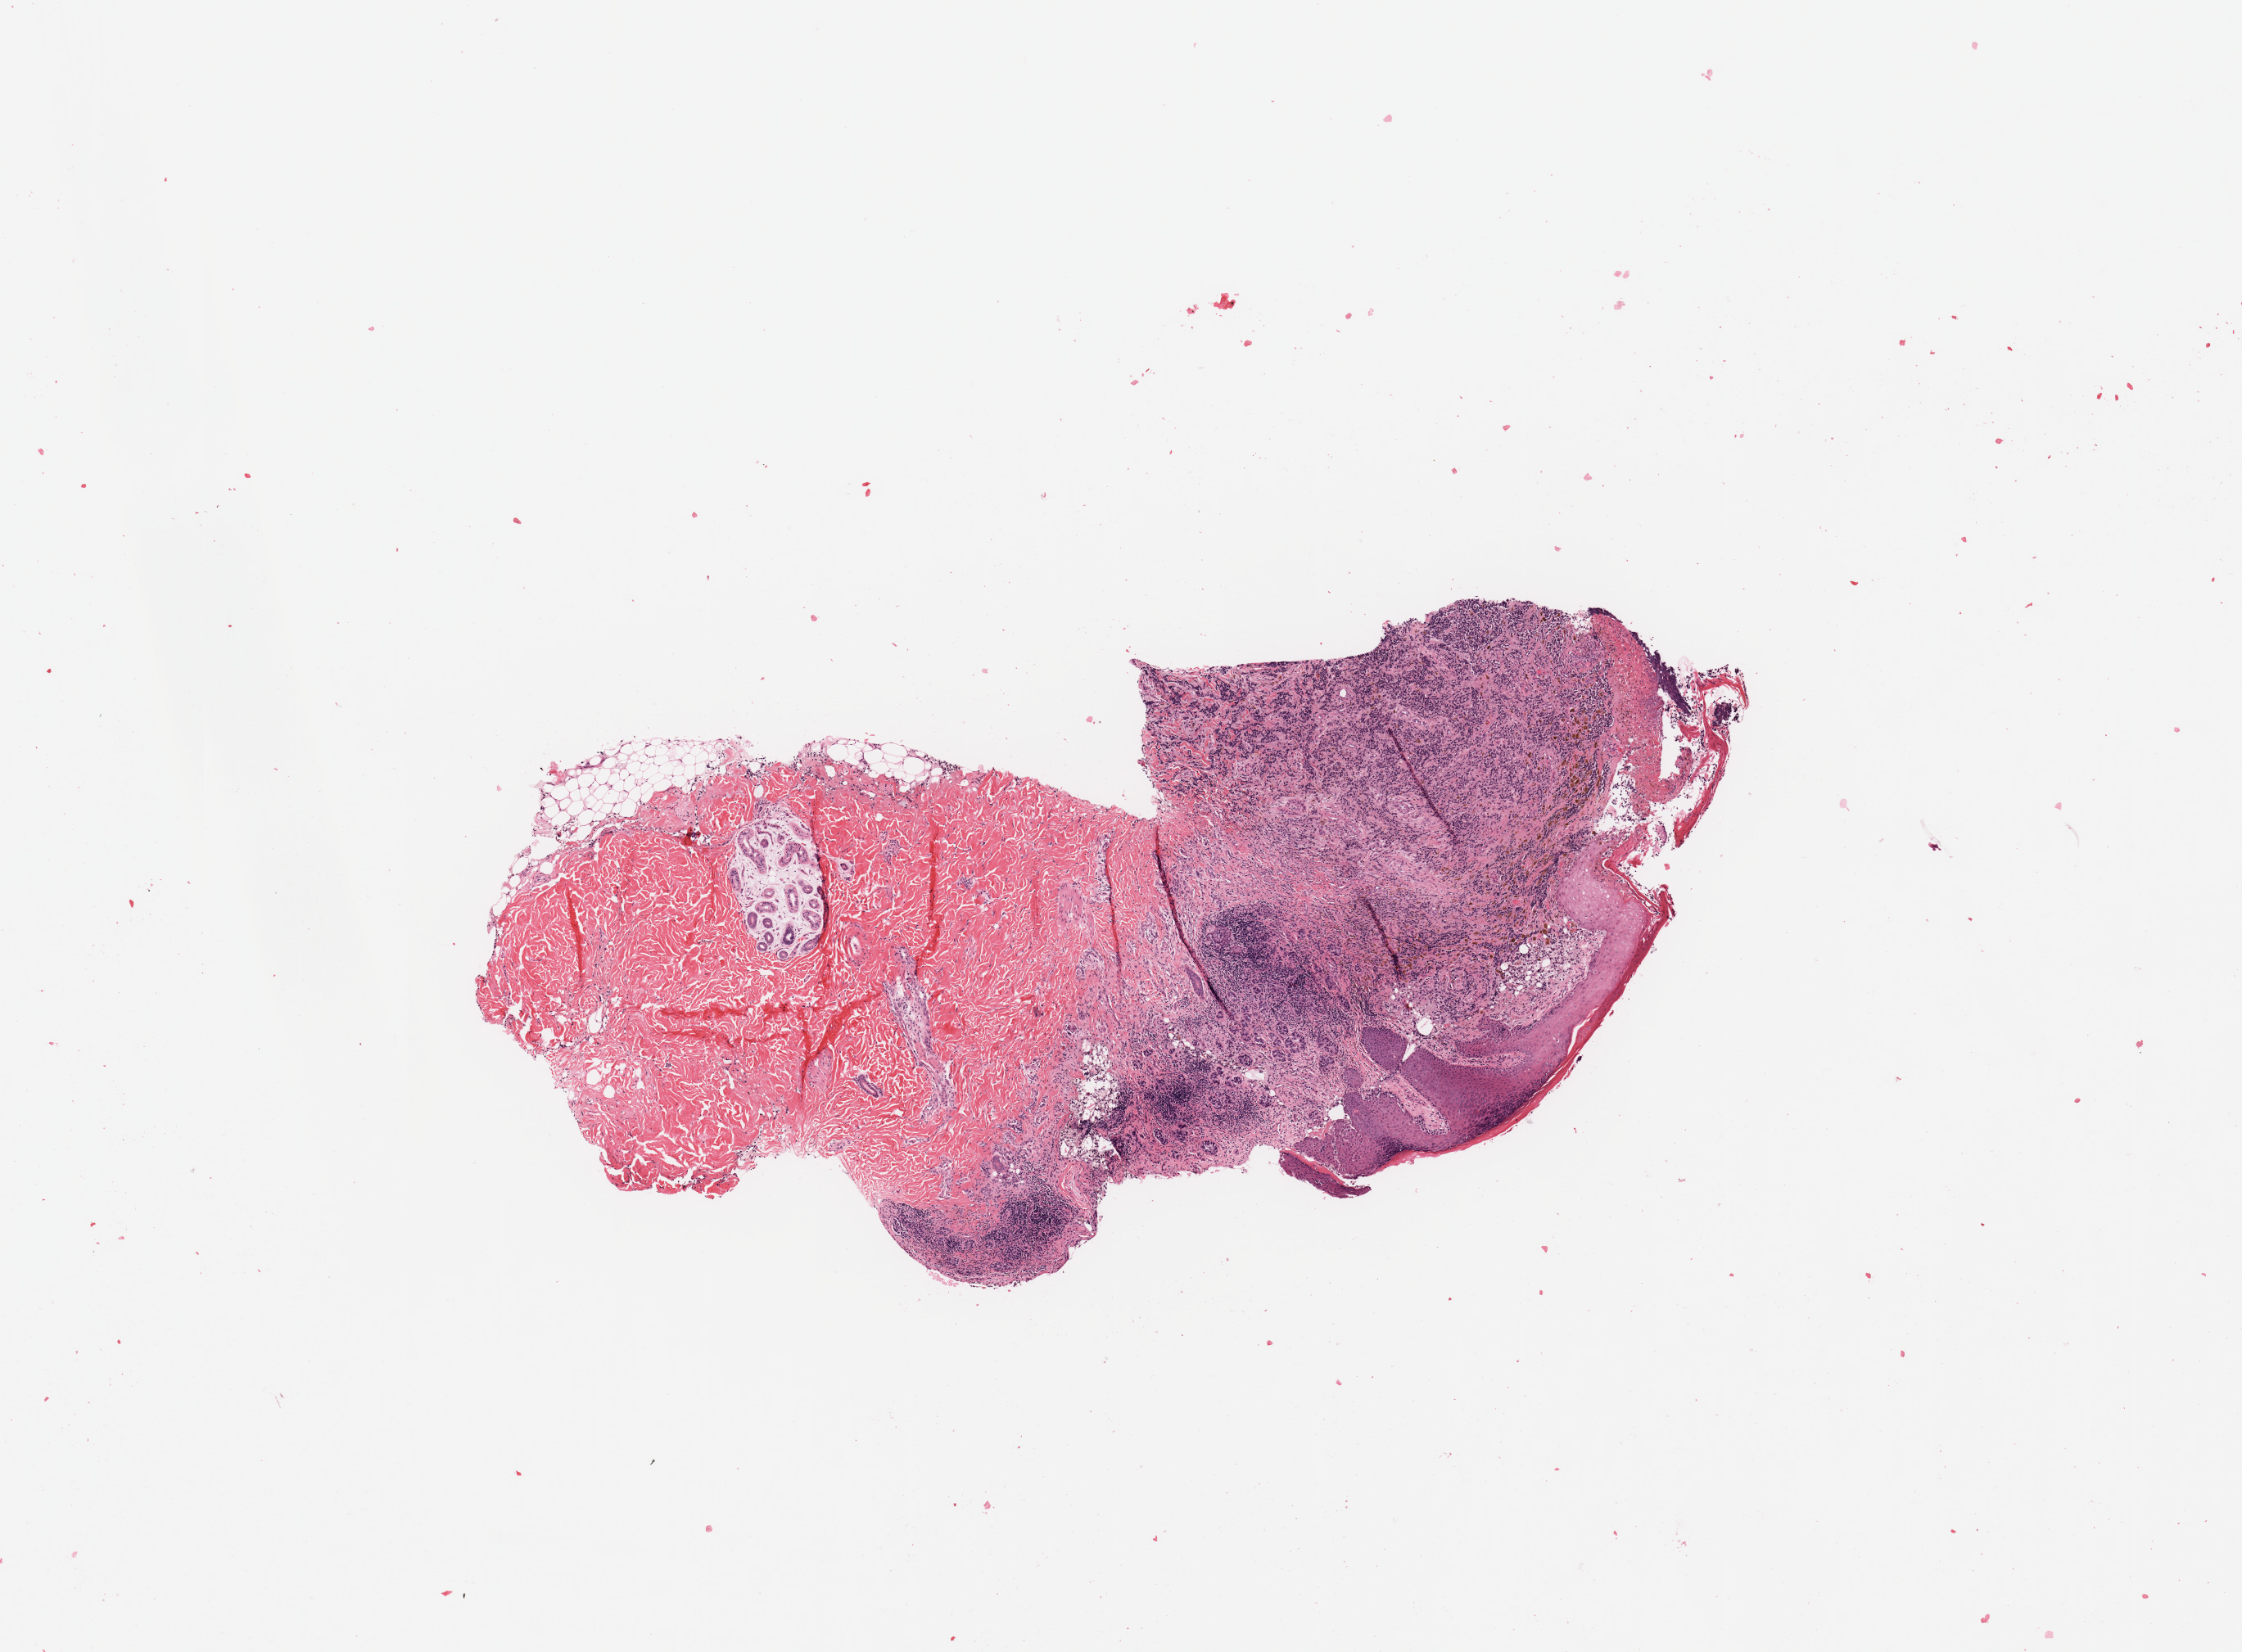
Digitized Hematoxylin and eosin (H&E) stained tissue section (whole slide) — whole scanned area (about 10.8 x 8.0 mm, acquisition: 20x scan) shown as a low-resolution overview. Melanoma tumour tissue; sampled site not recorded. 49-year-old female patient.
Diagnosis: Malignant melanoma, NOS.